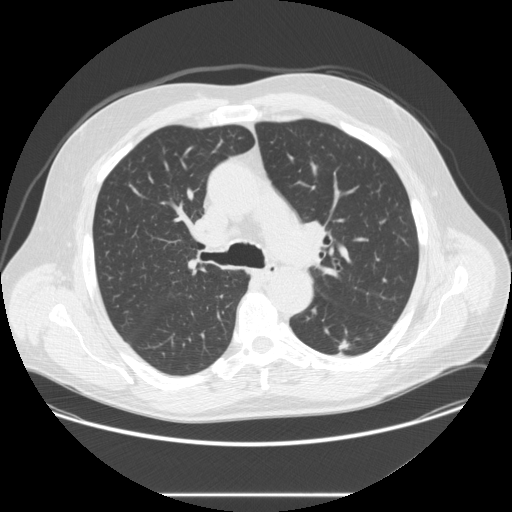
Low-dose screening chest CT, one axial slice; slice 169 of 262 in the series (ordered by position); 120 kVp; lung window (W 1500 / L -600 HU); 2.5 mm slice thickness; 512 × 512 image matrix, field of view 420 × 420 mm.
Structures marked on this image (outlined manually by an expert reader):
- lesion 1 (tumor, lower lobe of left lung): box from (x=338, y=340) to (x=350, y=355) px